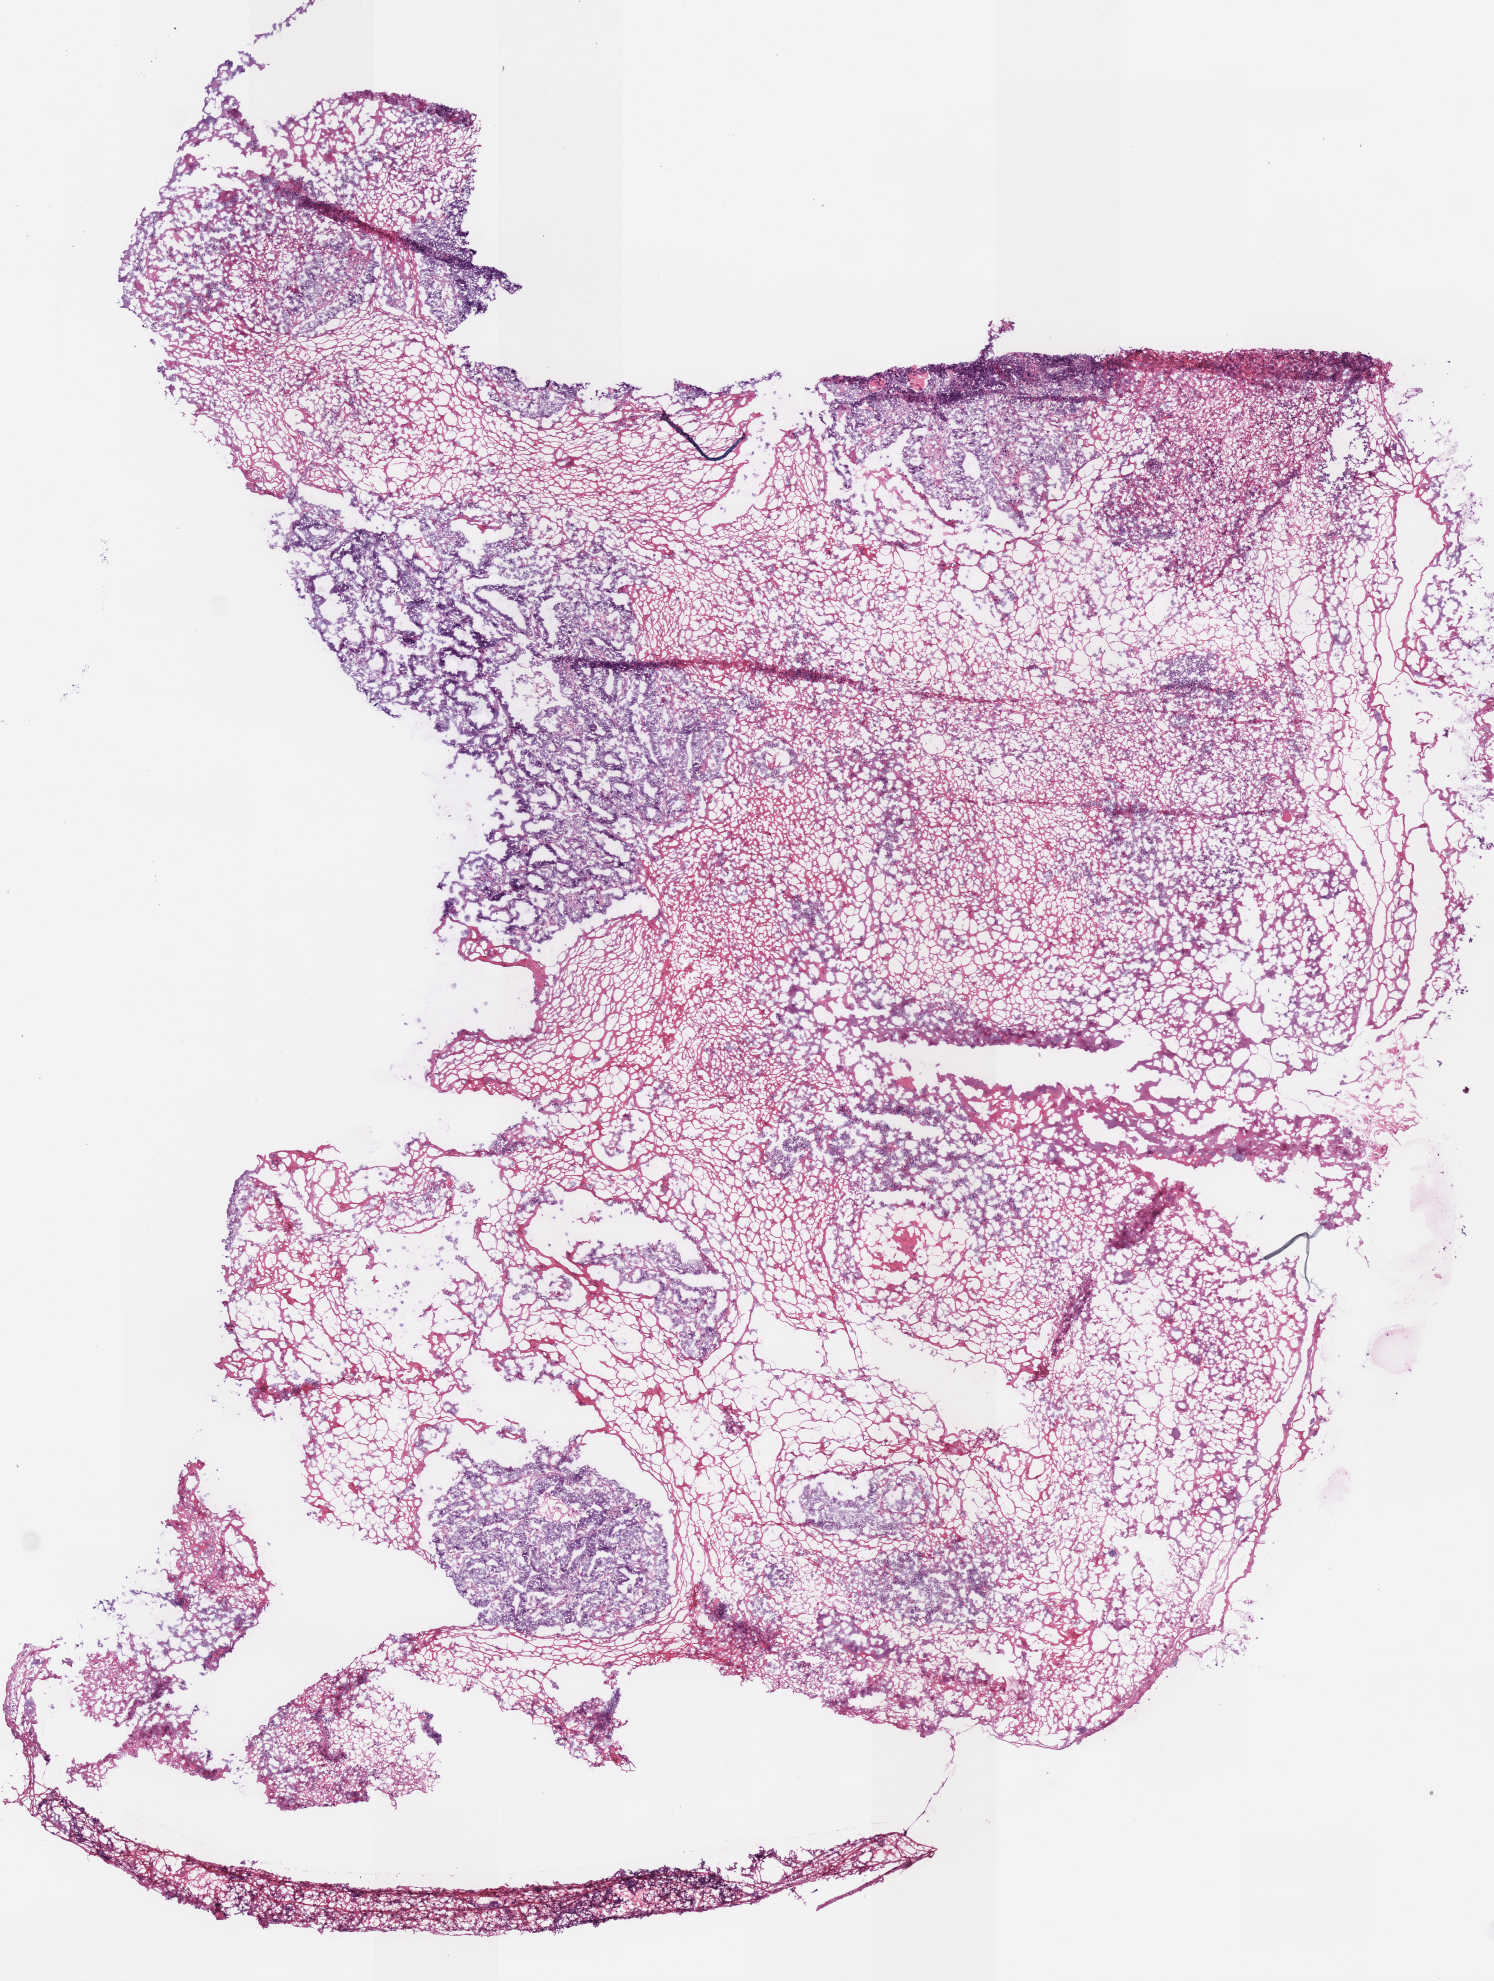
Digitized H&E-stained tissue section (whole slide) — whole scanned area (about 5.9 x 7.8 mm, acquisition: 40x scan) shown as a low-resolution overview, frozen section, primary tumour sample from the stomach. Male patient; age at initial diagnosis 75 years. Histologic grade: G2 (moderately differentiated). Slide review estimates, as recorded: tumour cells 60%, tumour nuclei 60%, normal cells 0%, stromal cells 40%, necrosis 0%.
- histologic diagnosis: Tubular adenocarcinoma (body of stomach)
- AJCC pathologic stage: IA (7th edition)
- lymph nodes positive (case pathology): 0 of 79 examined